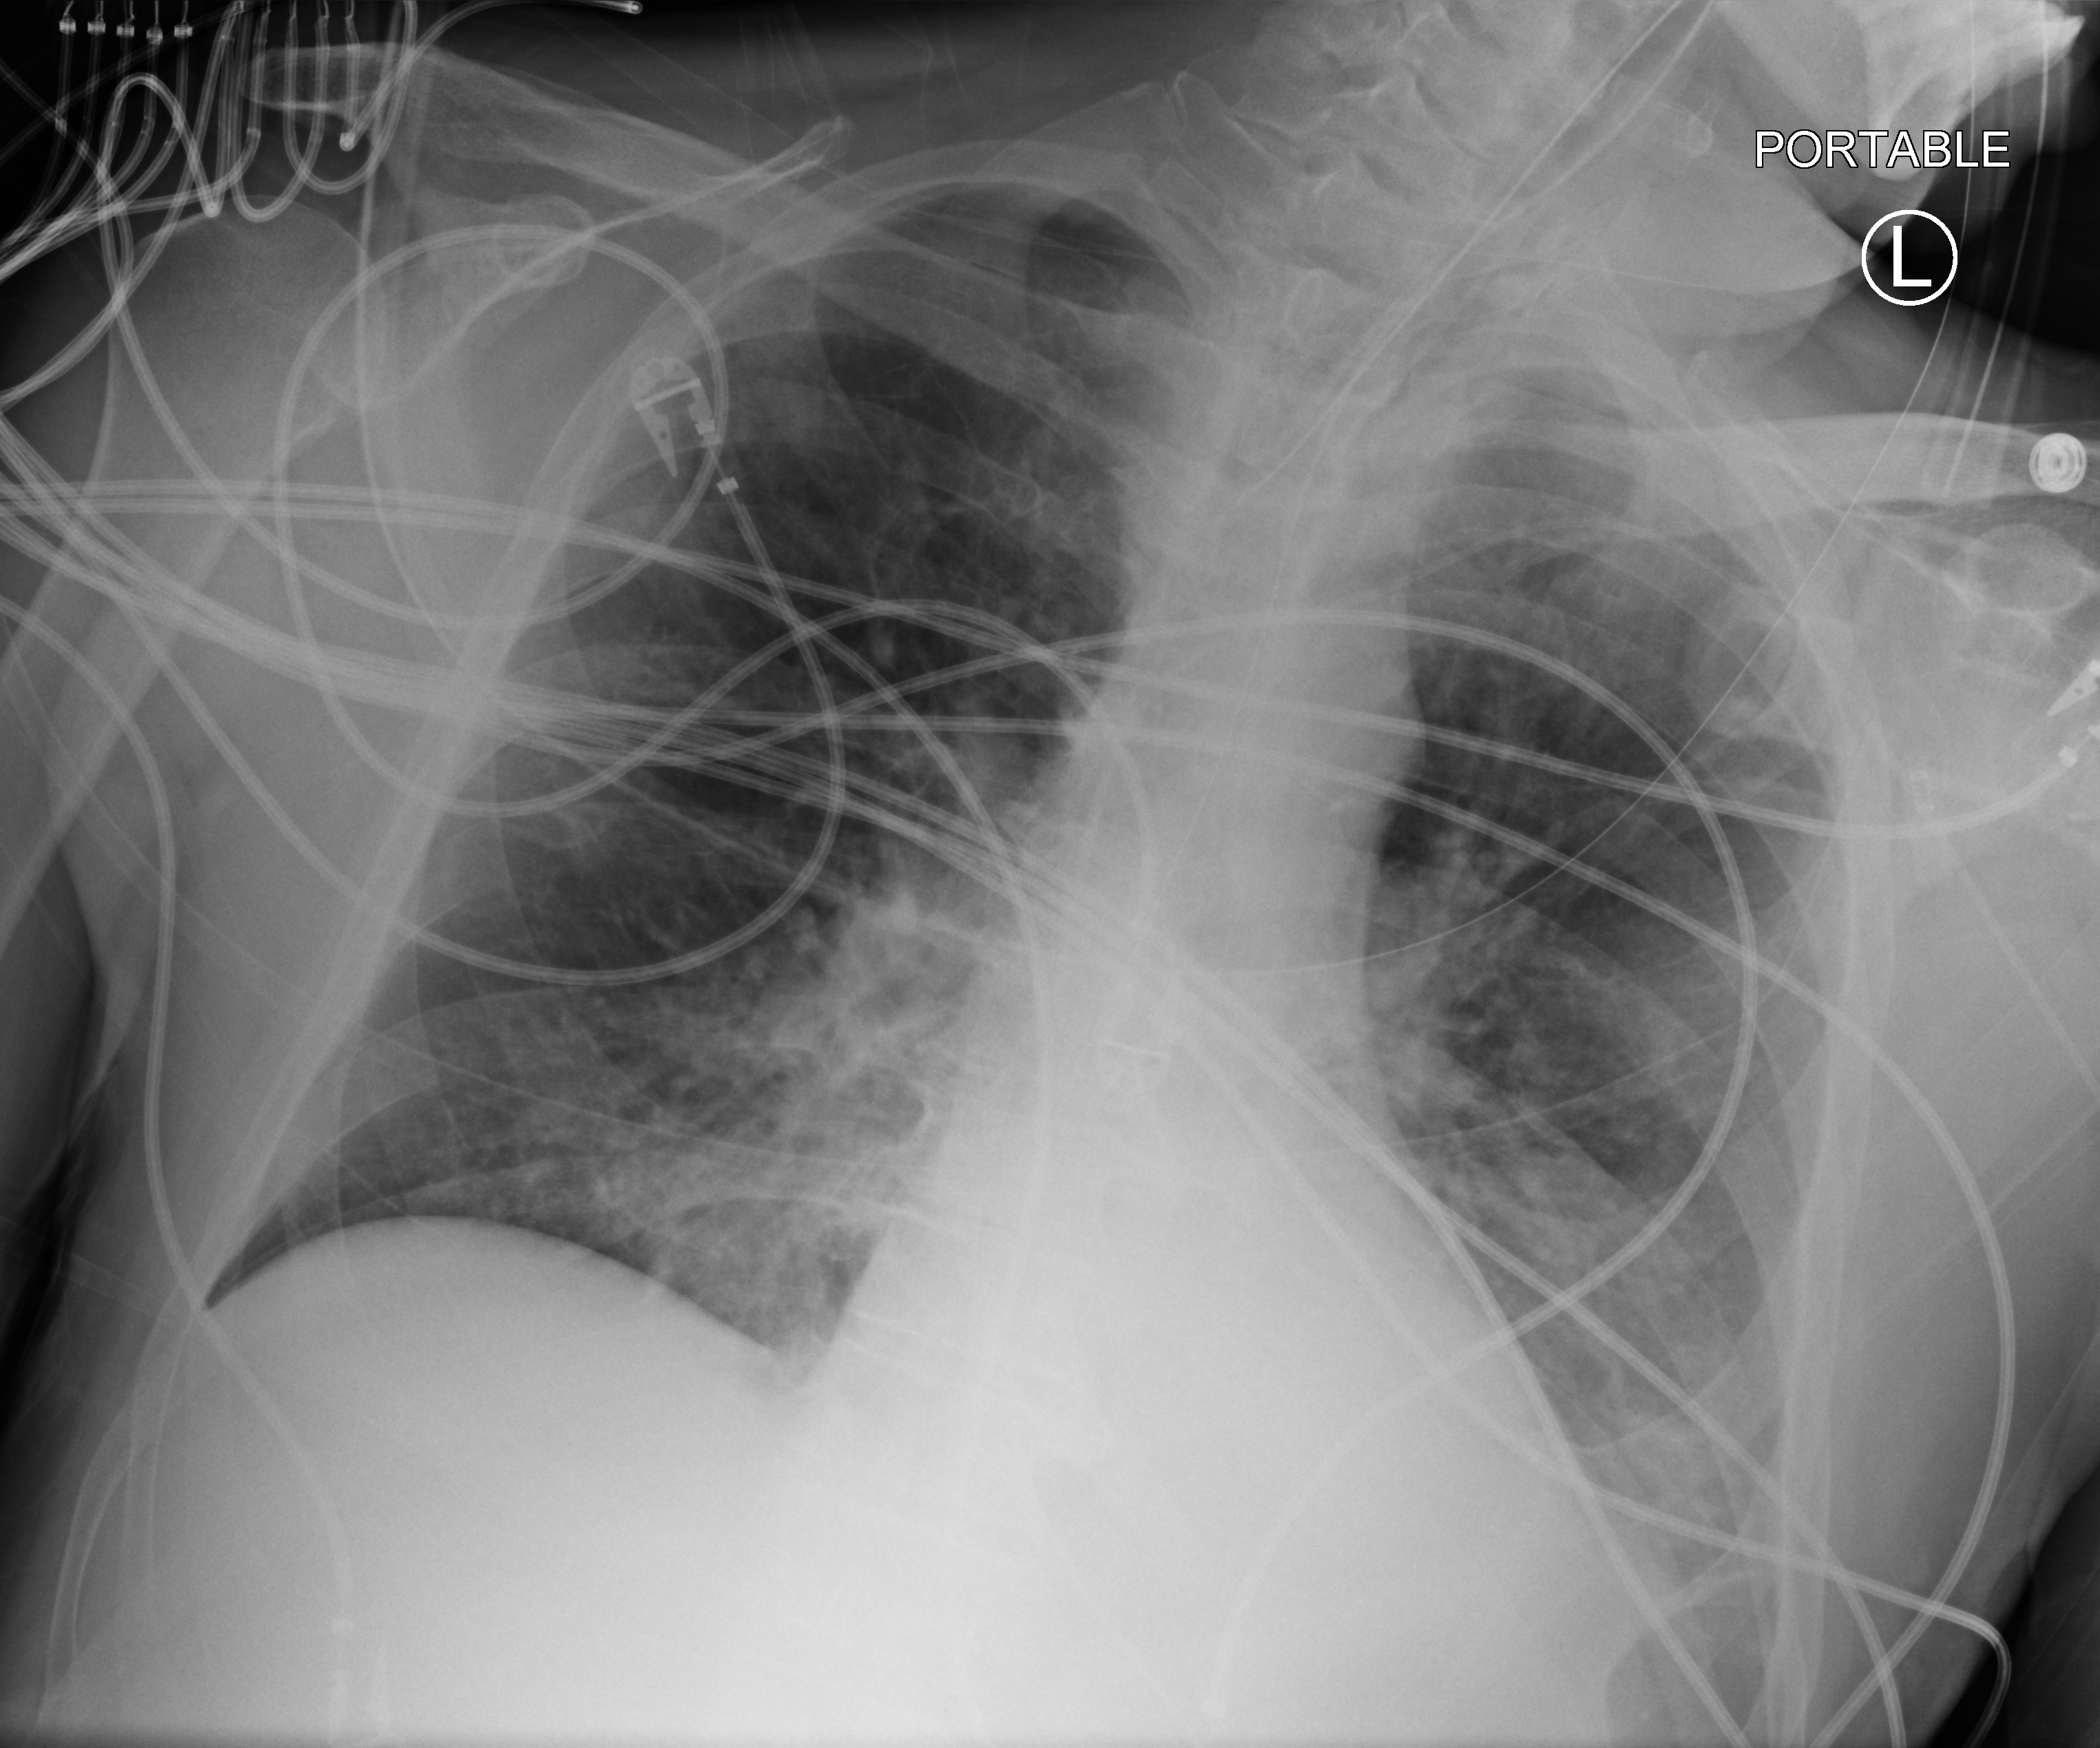
Portable chest radiograph. Patient hospitalised with COVID-19; male, aged 60–74 years.
Admission-level facts for this patient (not findings on this image; timing relative to this image not recorded):
- mechanically ventilated during this hospital stay: yes
- admitted to intensive care during this hospital stay: yes